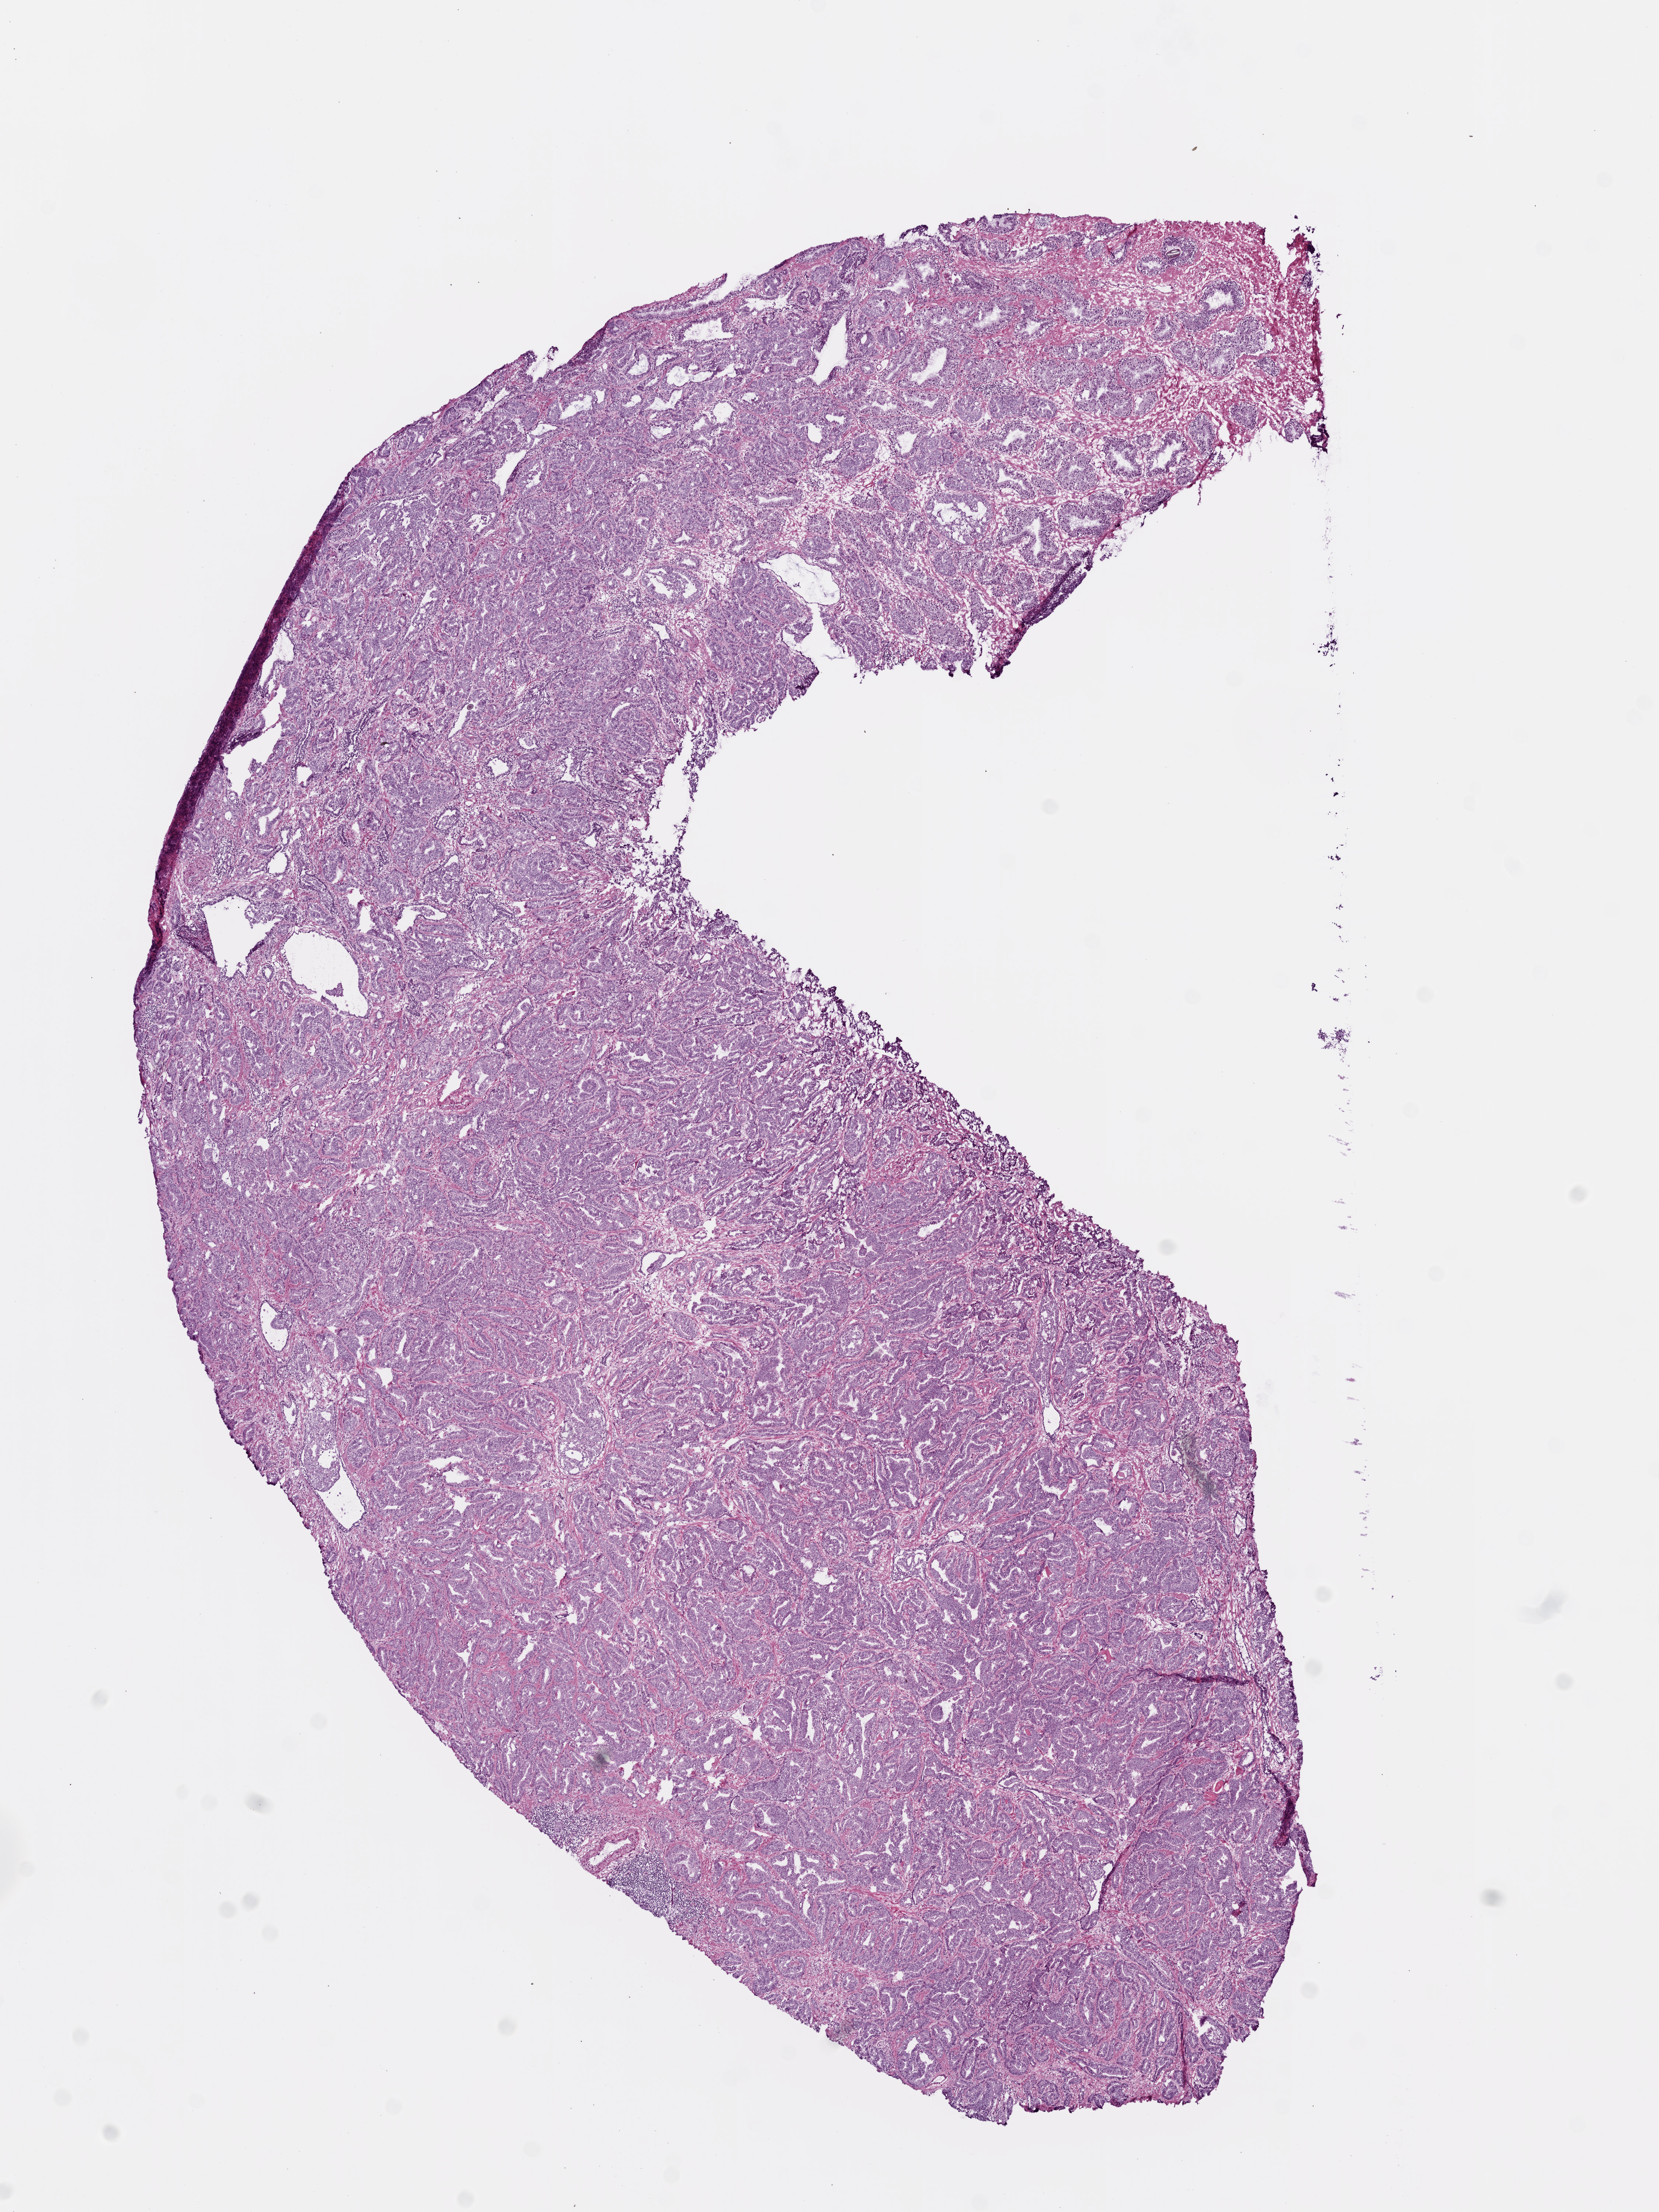
Hematoxylin and eosin (H&E) stained whole-slide image, low-resolution overview of the scanned area, about 9.0 x 12.0 mm. Frozen section from the top of the tissue portion. Sample: primary tumour, prostate. Patient: male, age at initial diagnosis 57 years. Gleason score: 7 (3+4). Slide review estimates, as recorded: tumour cells 90%, tumour nuclei 90%, normal cells 5%, stromal cells 5%, necrosis 0%. Infiltration values recorded for this section: lymphocyte infiltration 0%, monocyte infiltration 0%, neutrophil infiltration 0%.
* diagnosis: Acinar cell carcinoma (prostate gland)